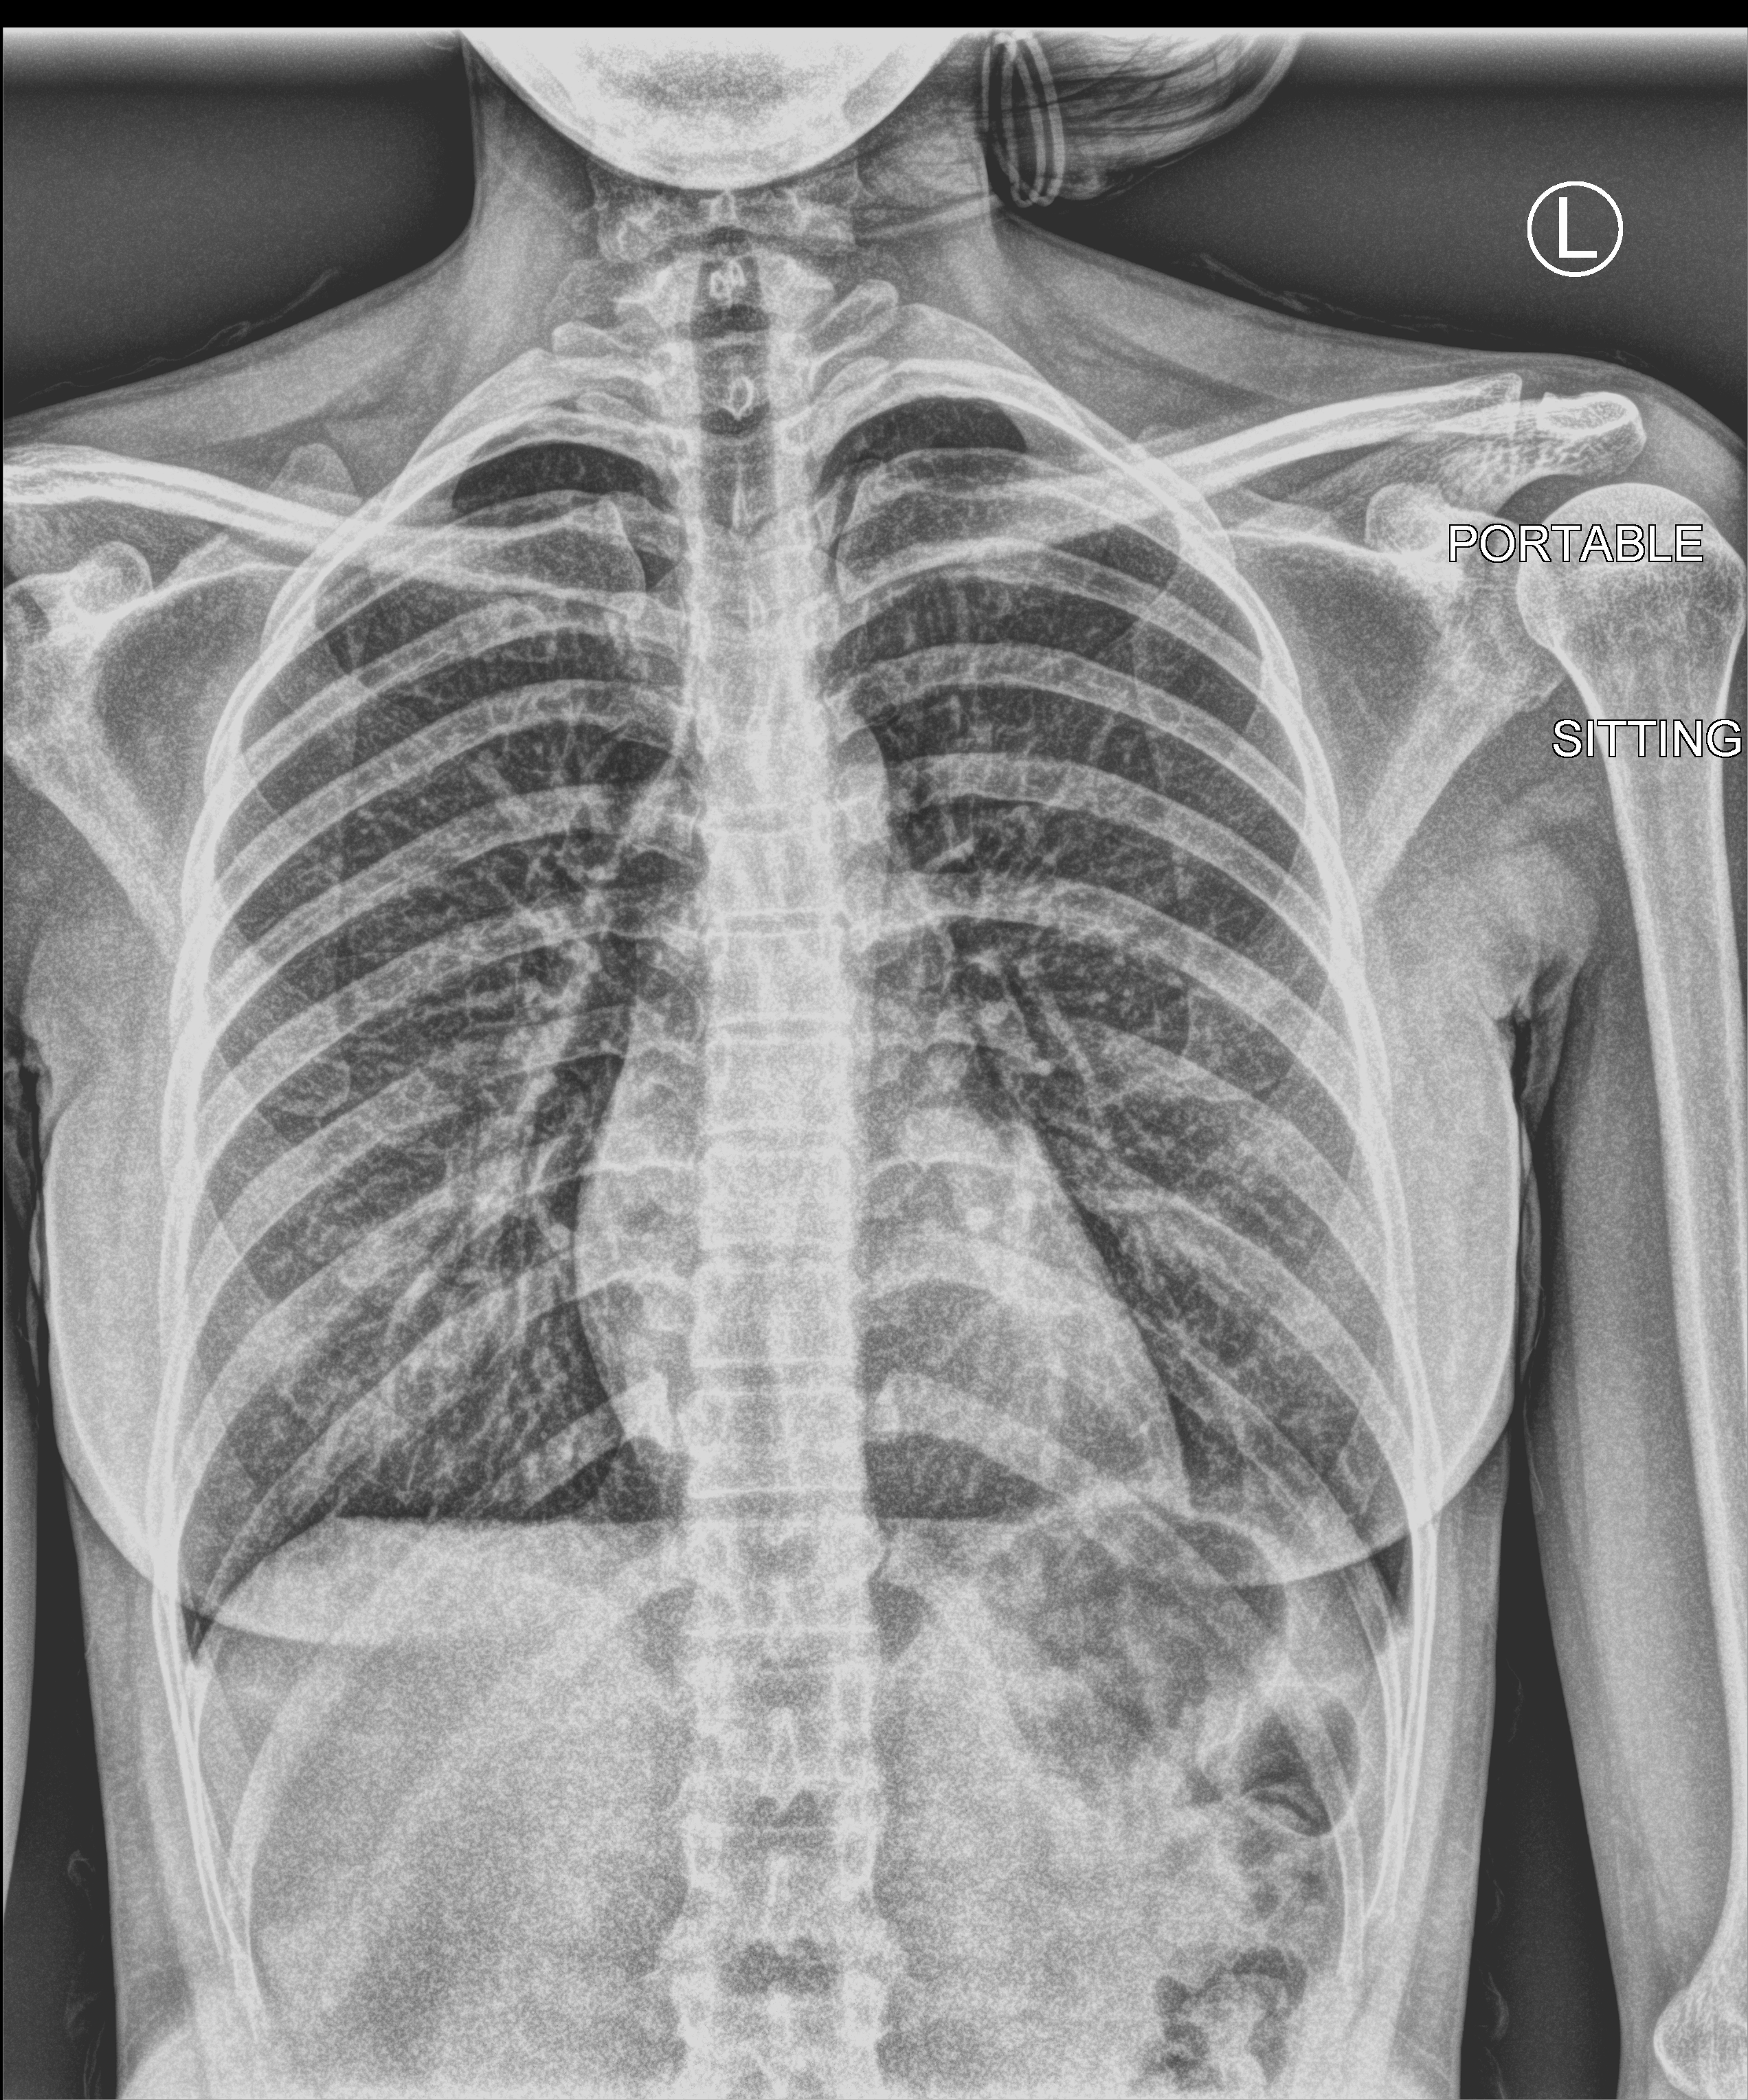
Chest X-ray (portable), anteroposterior (AP) projection. Female patient hospitalised with COVID-19, age 18–59 years.
From the hospital-stay record, not from the radiograph (when in the stay this image was taken is not recorded): COPD (admission record): no.